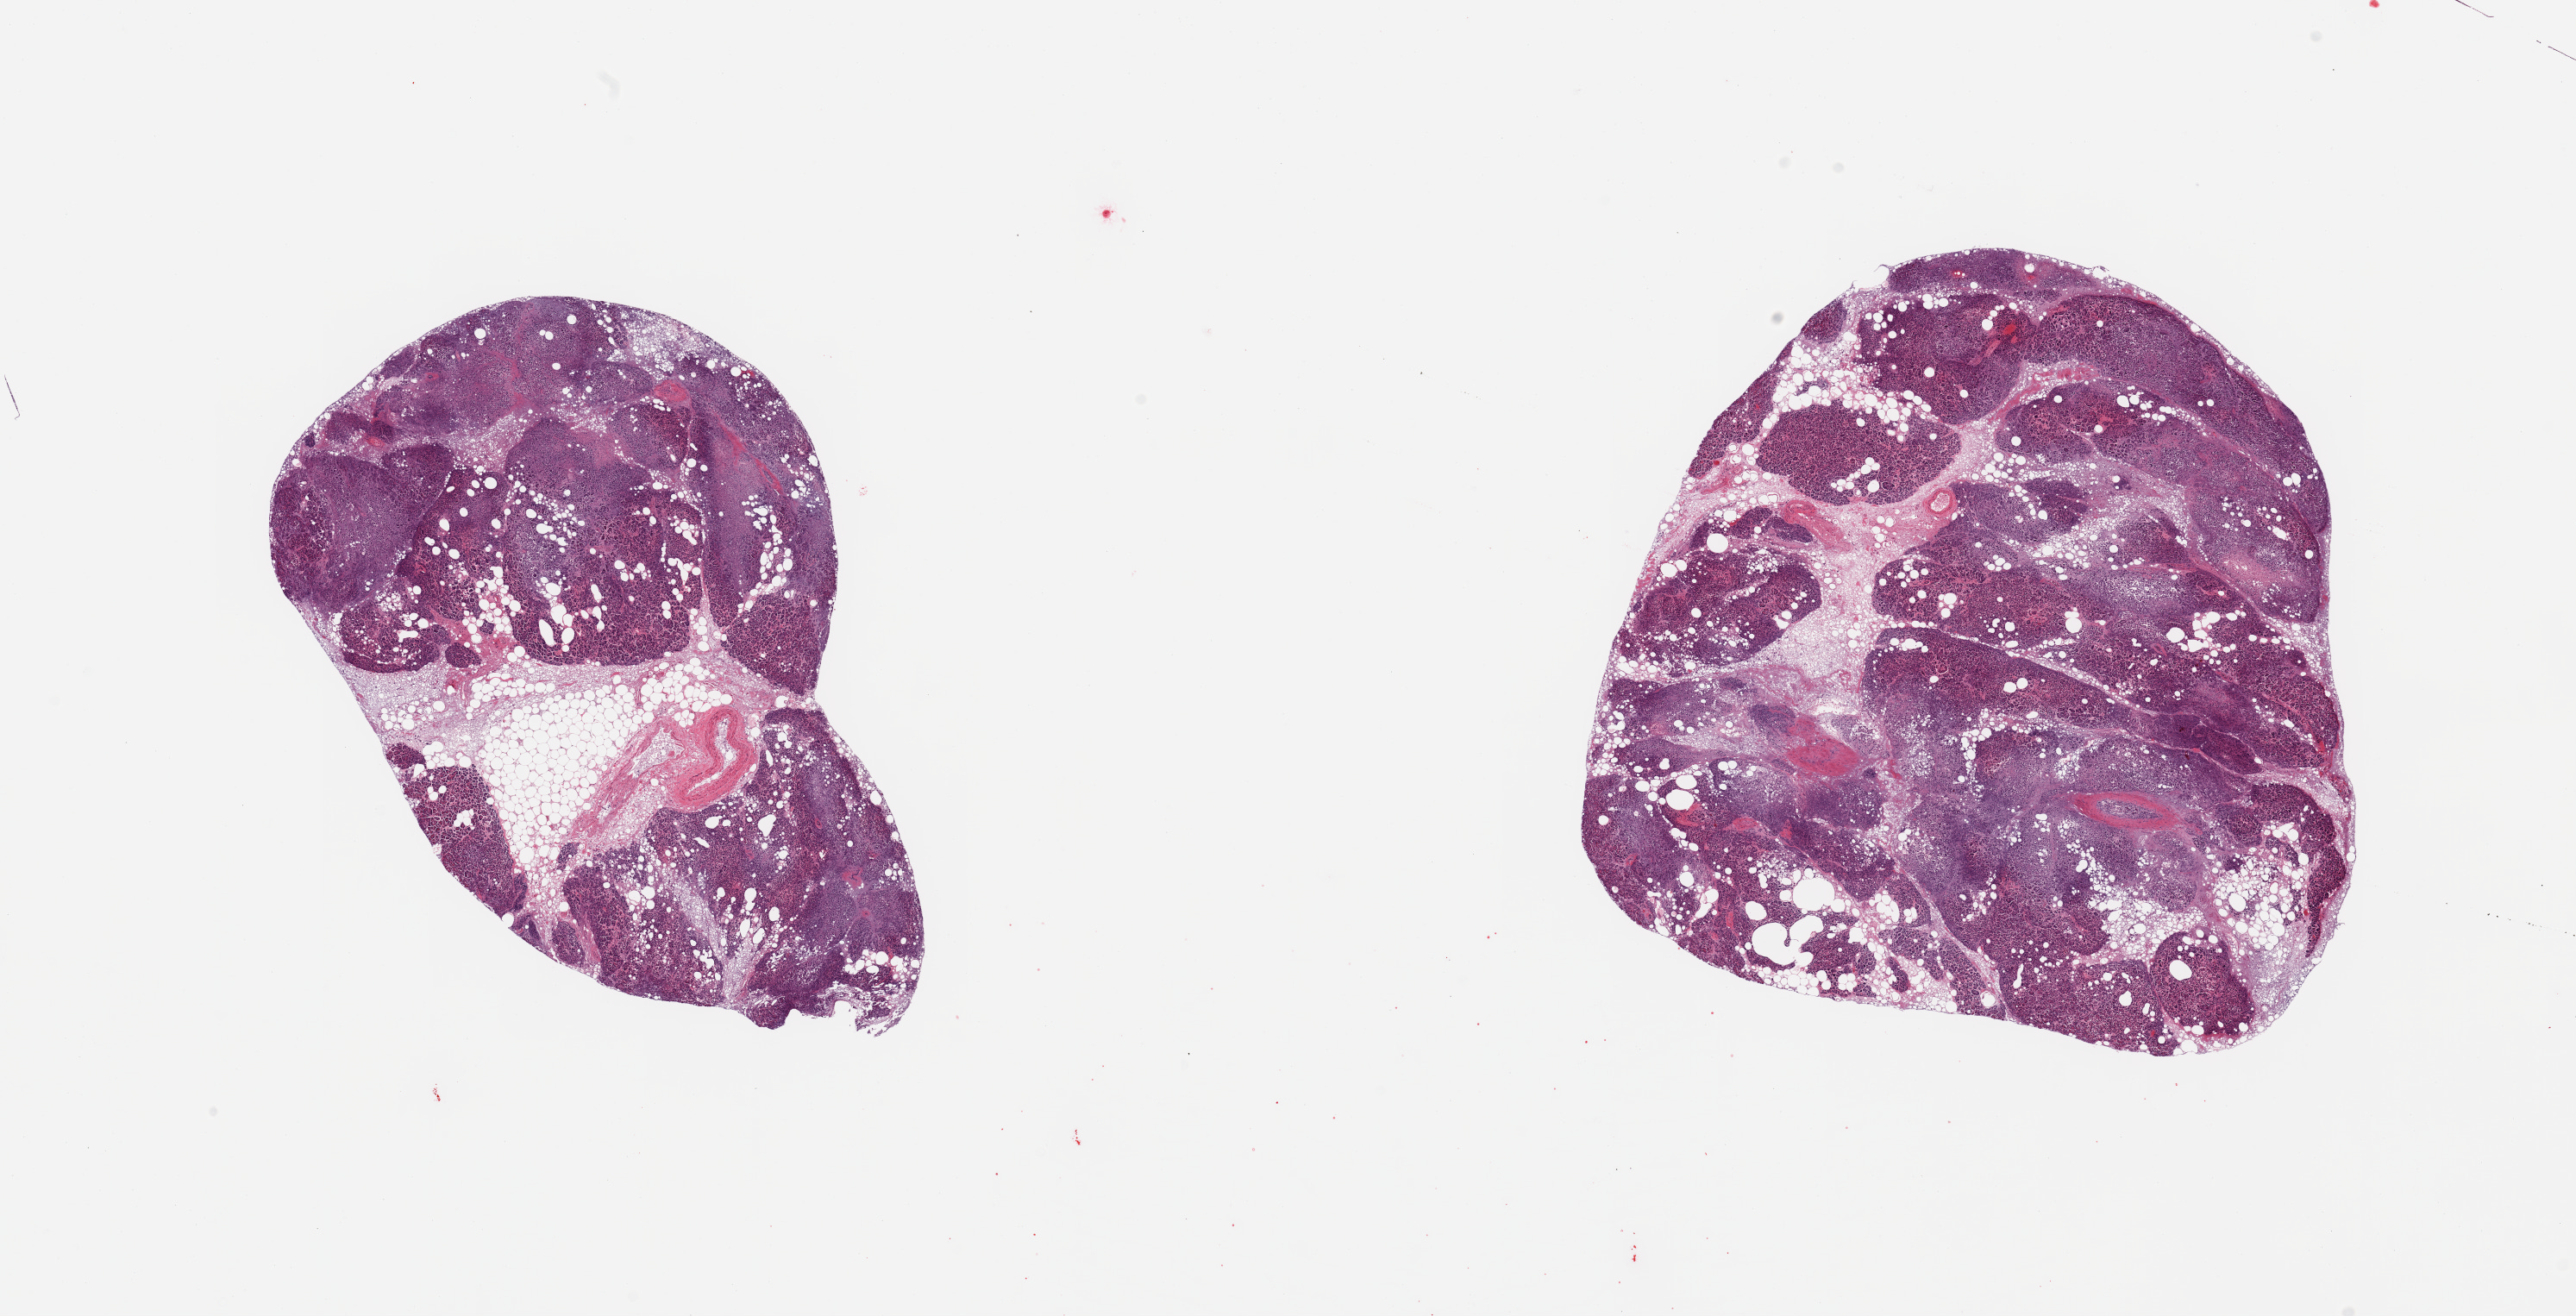
H&E whole-slide image, brightfield — low-resolution overview of the scanned area, about 23.6 x 12.1 mm; PAXgene-fixed, paraffin-embedded tissue; target tissue: pancreas; donor tissue sample. Donor: male.
Review note (as recorded): 2 pieces; 40% autolyzed parenchyma grade 3; 30% parenchymal grade 2; internal fat 30%, partly grade 3 autolyzed.